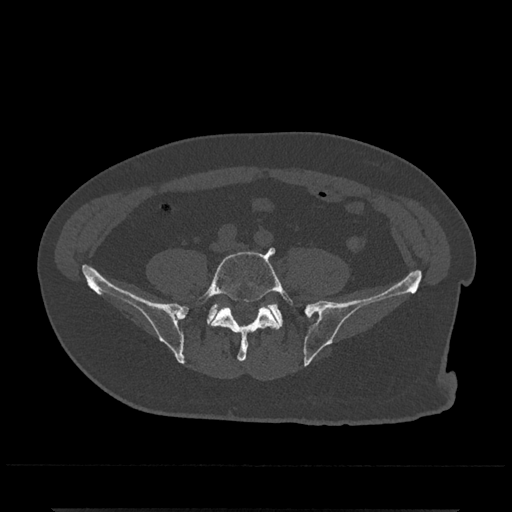
CT including the spine, one axial slice. Slice 78 of 797 in the series (ordered by position). Reconstruction kernel Br40s/3. 120 kVp. Bone window (W 1800 / L 400 HU). 0.5 mm slice thickness. 512 × 512 image matrix, field of view 393 × 393 mm. Patient: male, 67 years. From the clinical record (not read from this slice): primary cancer: prostate.
Annotated regions visible in this slice (semi-automatically segmented with operator editing):
- L5 vertebra: bounding box [x1, y1, x2, y2] px = [196, 247, 294, 362]